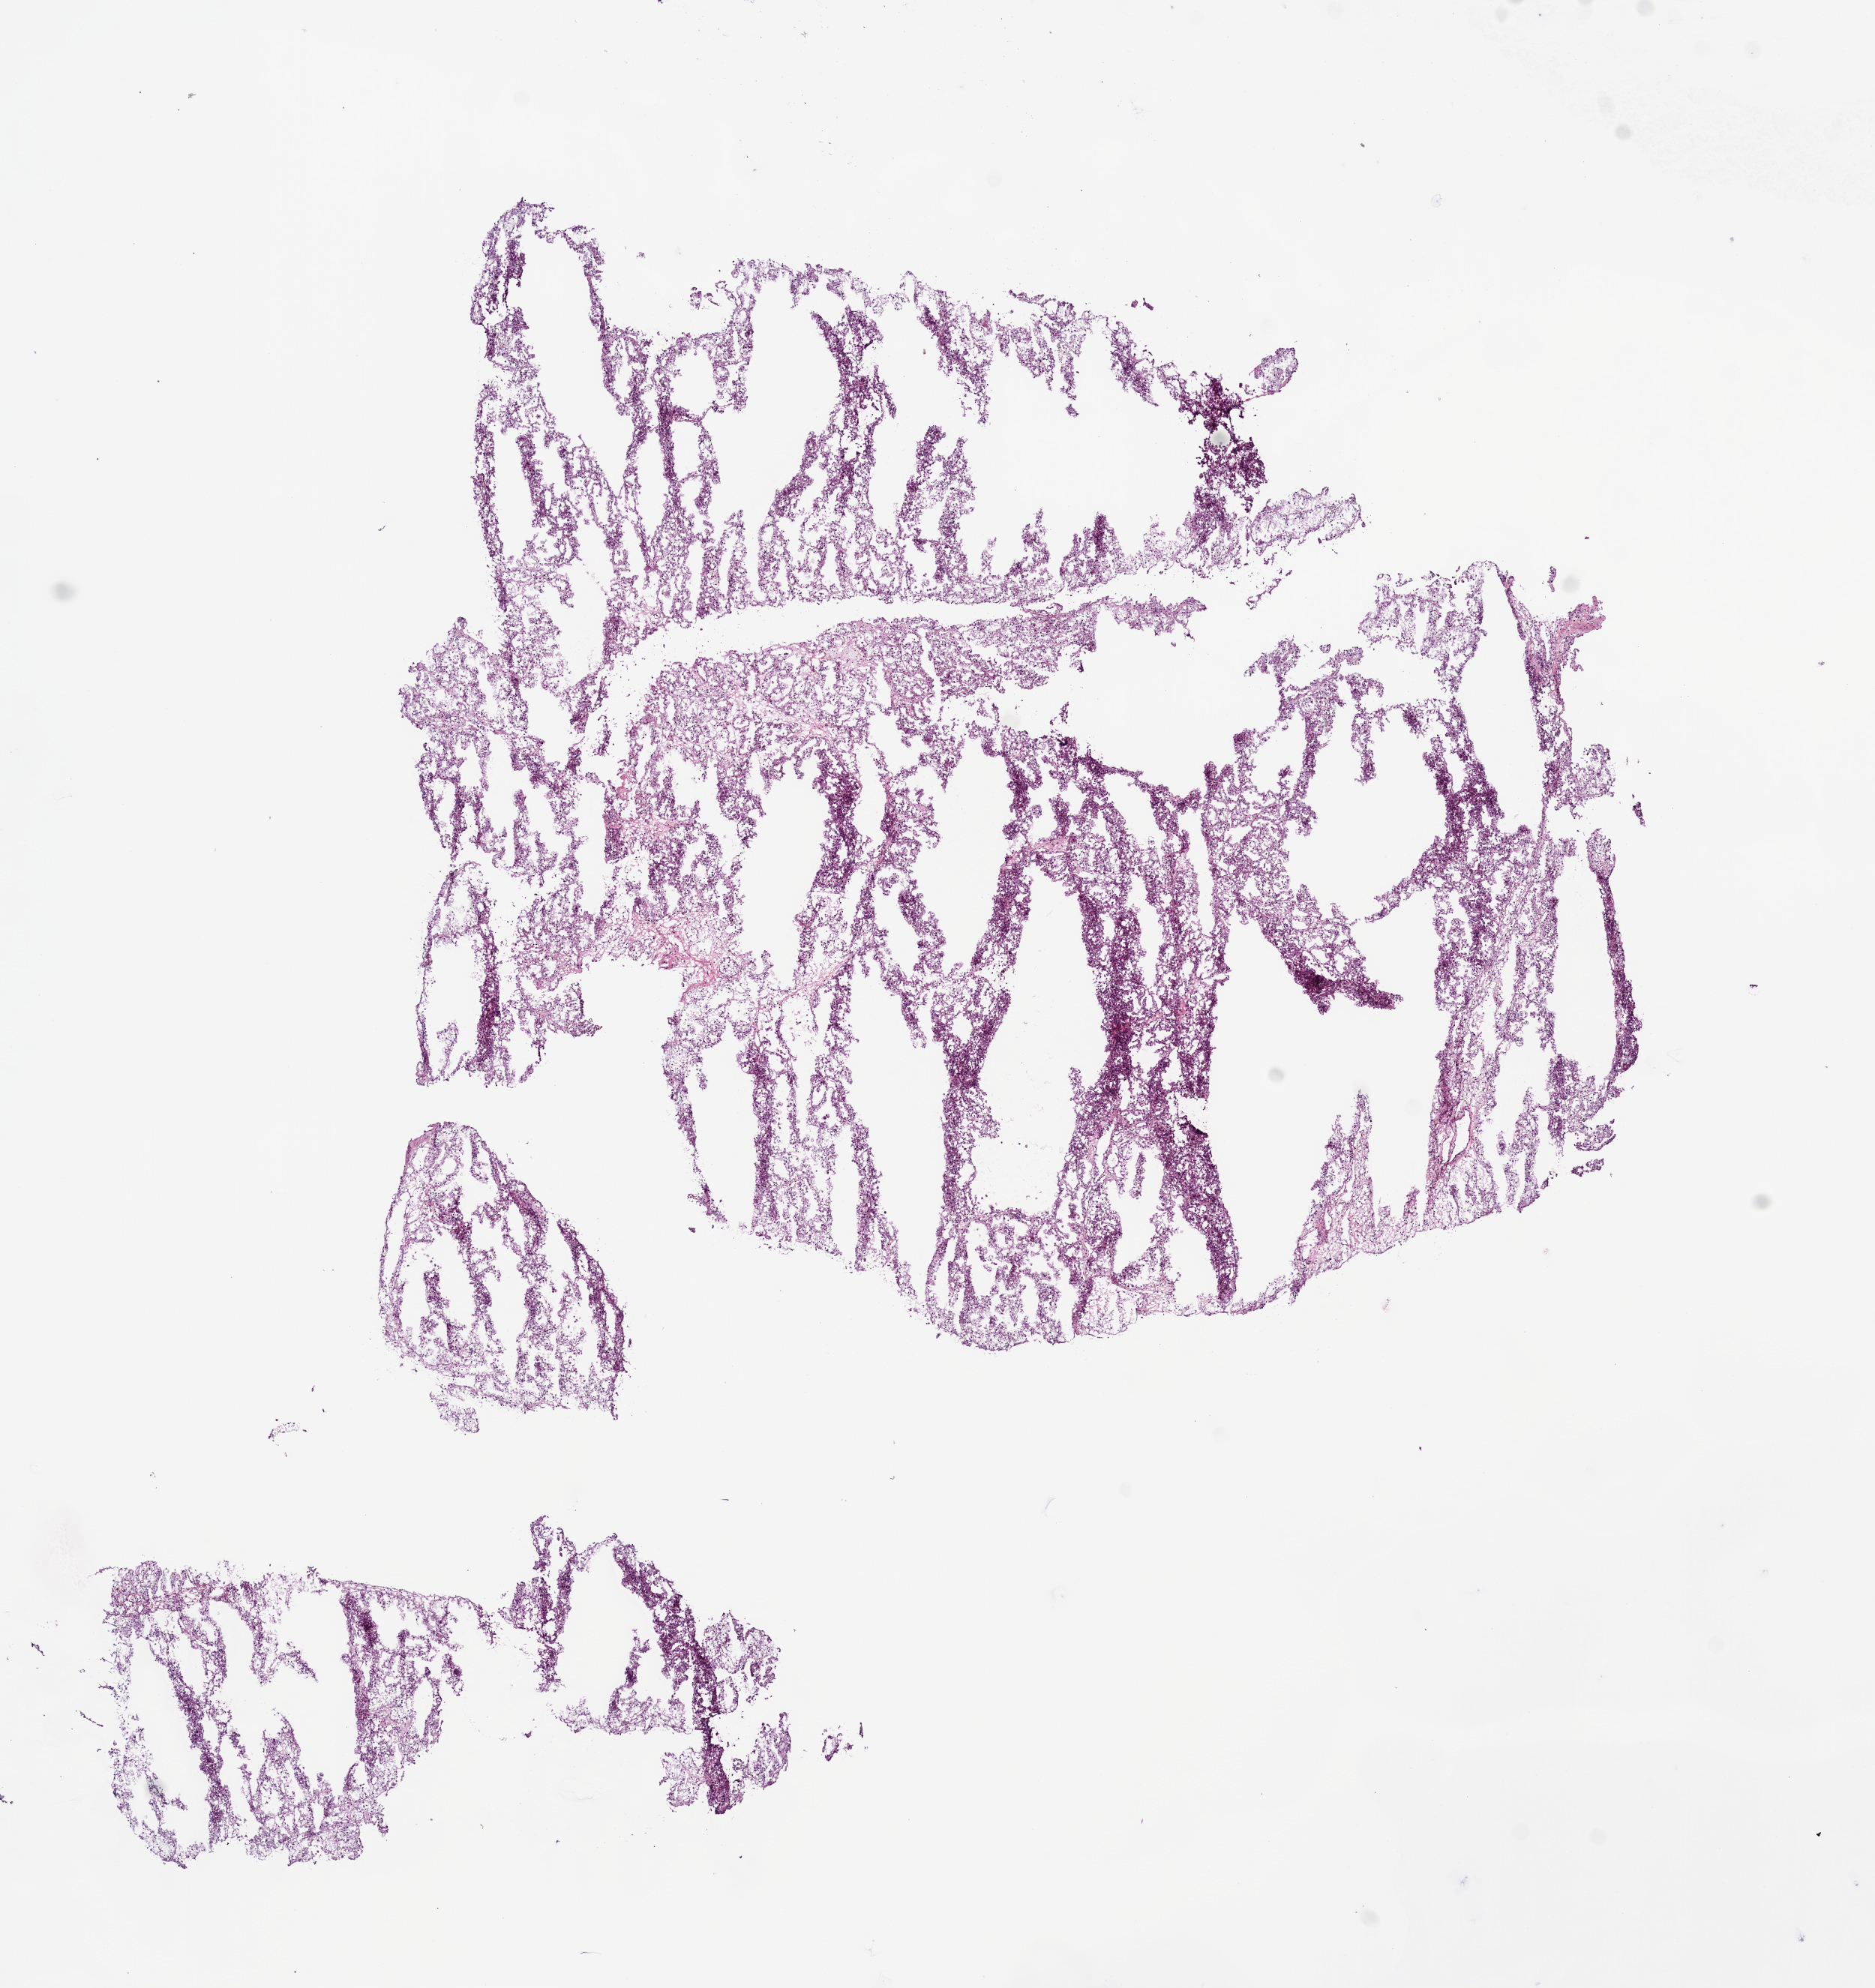
Digitized H&E tissue section (whole slide), a low-resolution overview of the entire scanned area, about 10.0 x 10.6 mm (from a 20x scan), frozen section from the bottom of the tissue portion, sample: primary tumour, kidney. Patient: female, age at initial diagnosis 45 years. Histologic grade: G2 (moderately differentiated). Composition of this section per pathologist review: tumour cells 95%, tumour nuclei 85%, normal cells 0%, stromal cells 5%, necrosis 0%.
TNM: T1a NX M0. AJCC pathologic stage: I. Histologic diagnosis: Clear cell adenocarcinoma, NOS.